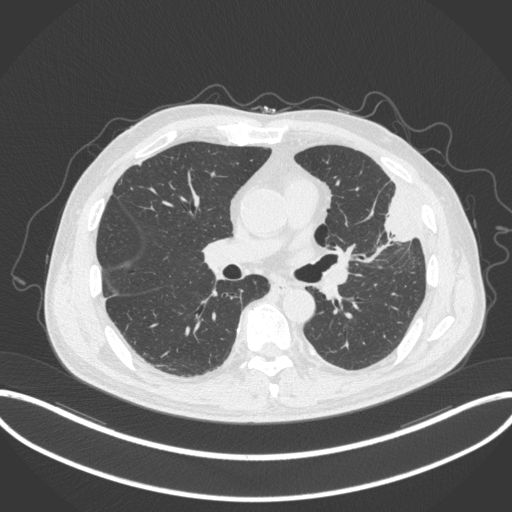
Chest CT, one axial slice. Slice 182 of 382 in the series (ordered by position). Reconstruction kernel B31f. Lung window (W 1500 / L -600 HU). 1 mm slice thickness. 512 × 512 image matrix, field of view 415 × 415 mm. Male patient, age 64 years. From the clinical record (not read from this slice): clinical TNM (as recorded): T4 N1 M0; histopathological grade: G3.
Structures marked on this image (bounding box drawn by a radiologist):
- lung tumour (recorded histology: adenocarcinoma): box from (x=380, y=182) to (x=419, y=246) px